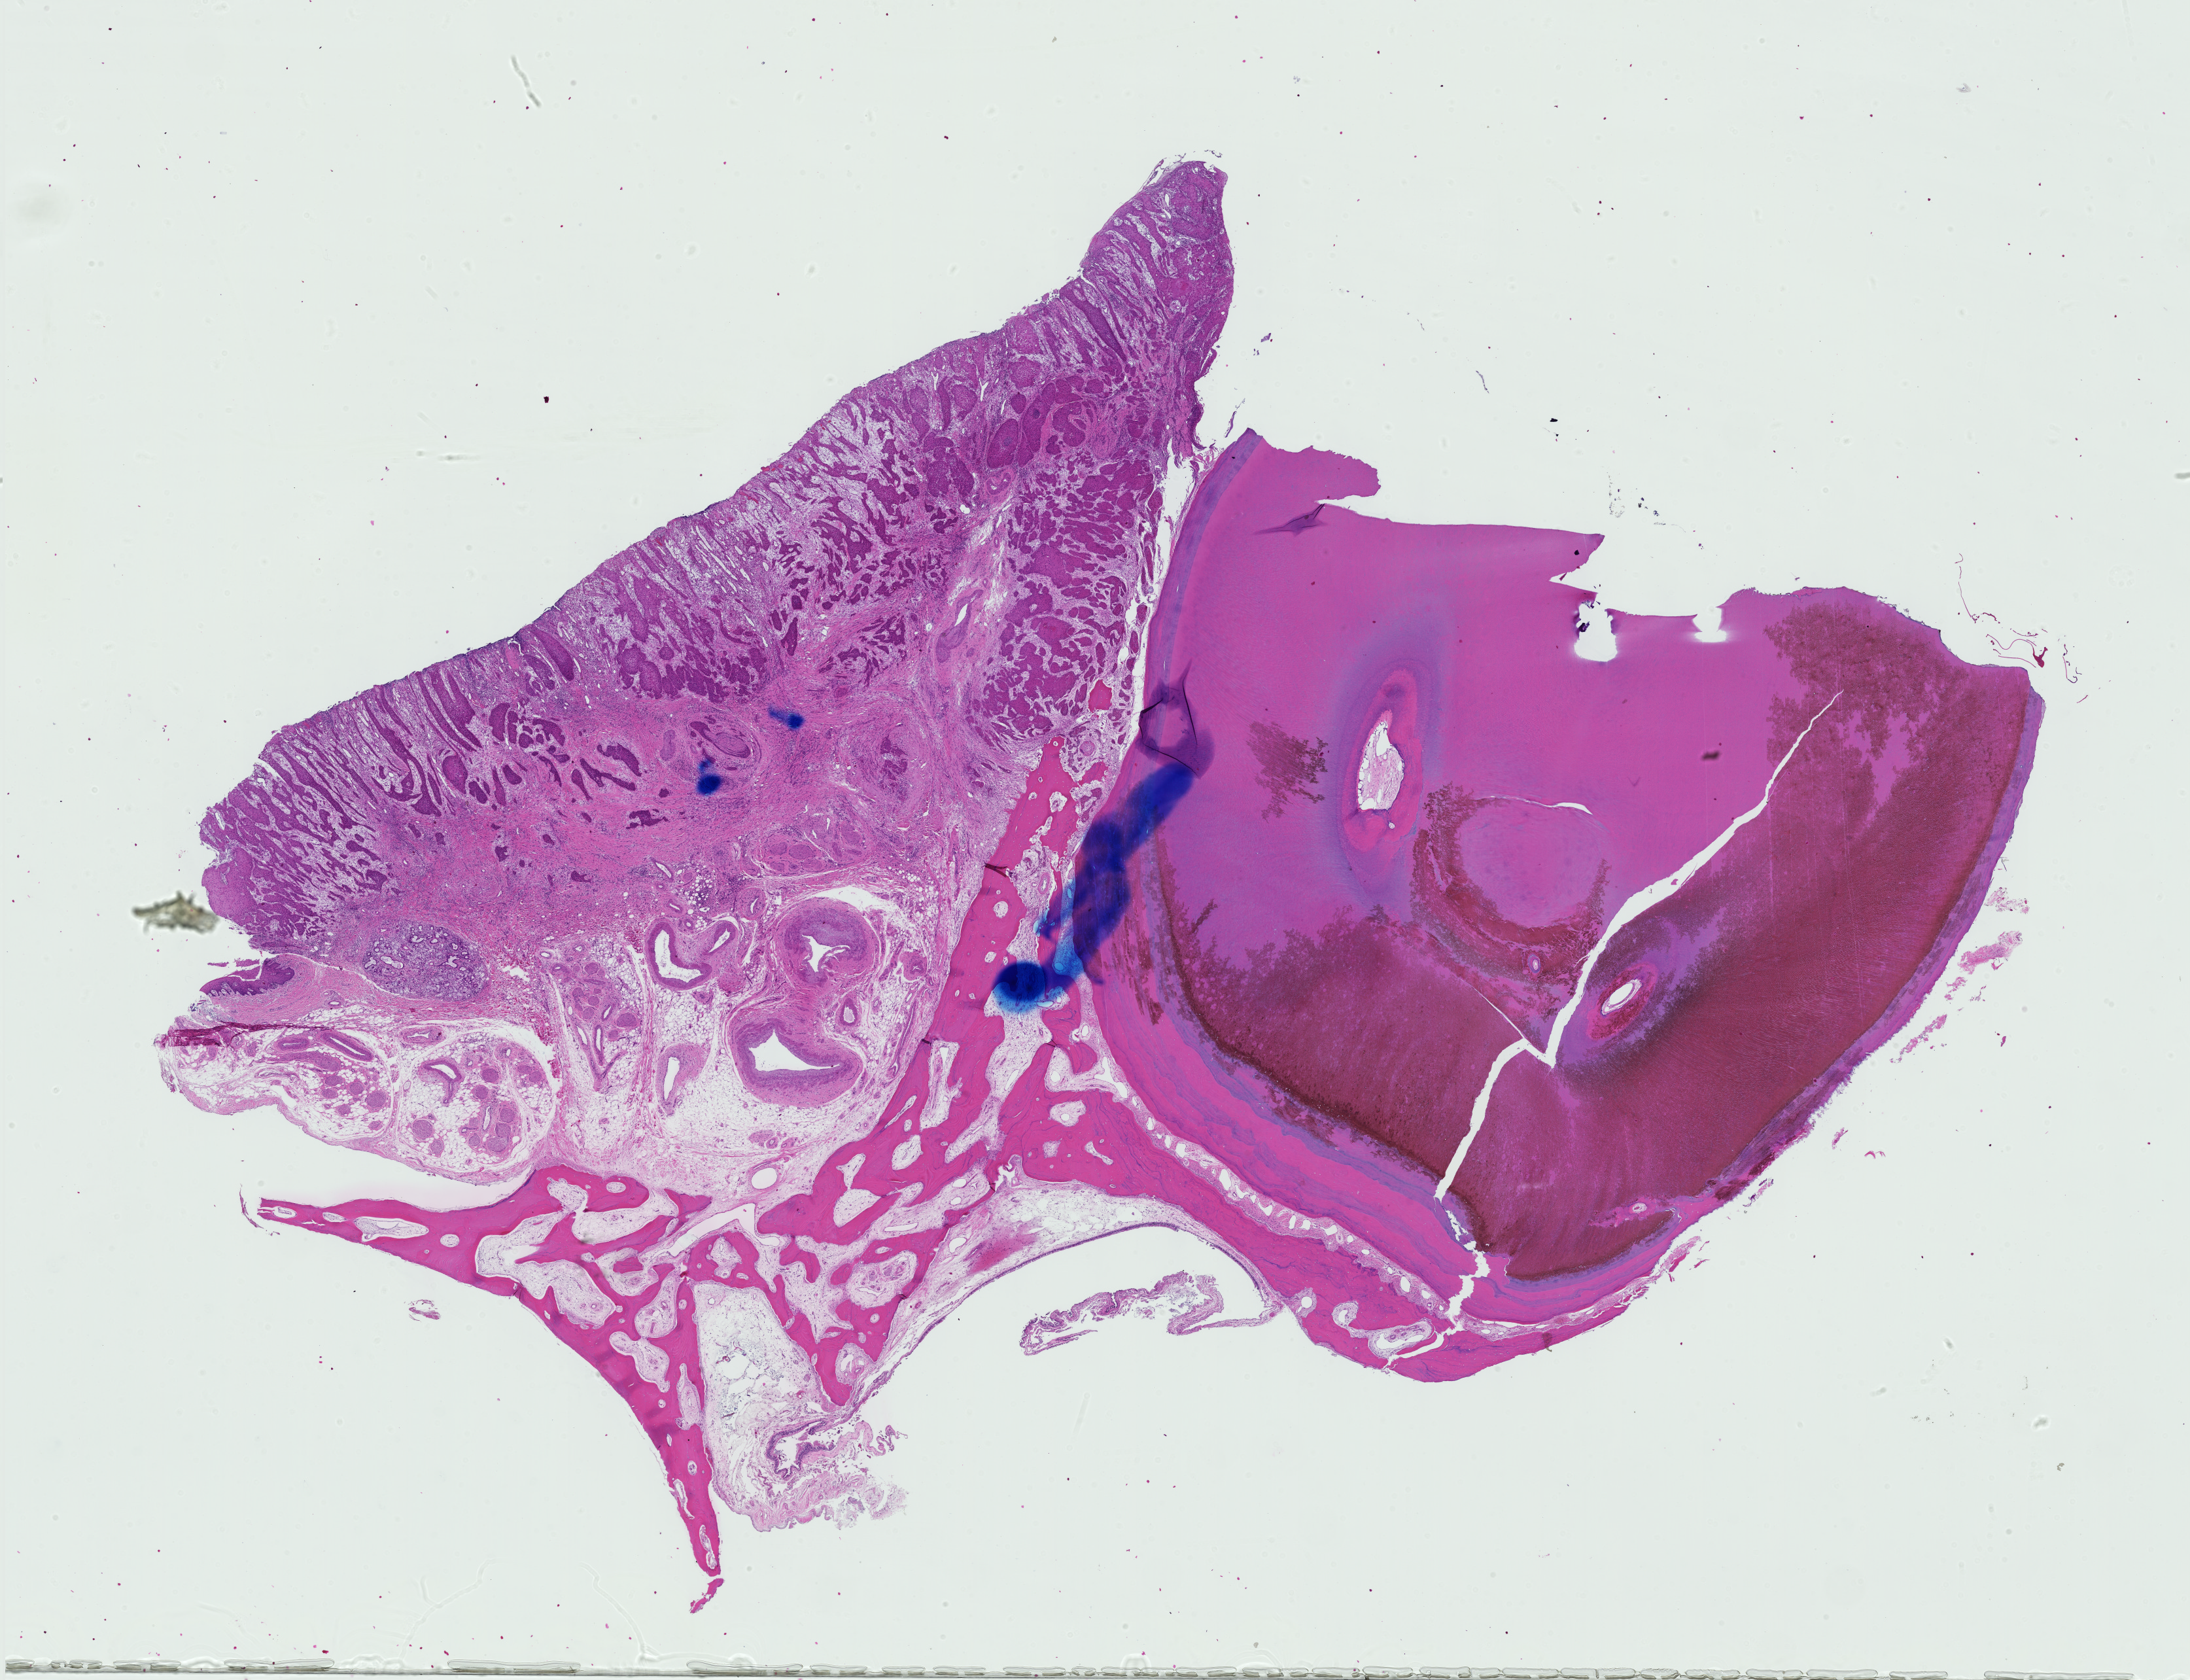
H&E-stained whole-slide image, shown as a low-resolution overview of the whole scanned area (about 24.3 x 18.6 mm), FFPE section, head and neck, primary tumour sample. Patient: female, age at initial diagnosis 79 years. Histologic grade: G1 (well differentiated).
• pathologic diagnosis: Squamous cell carcinoma, NOS (floor of mouth, NOS)
• AJCC pathologic stage: IVA (7th edition)
• laterality: right